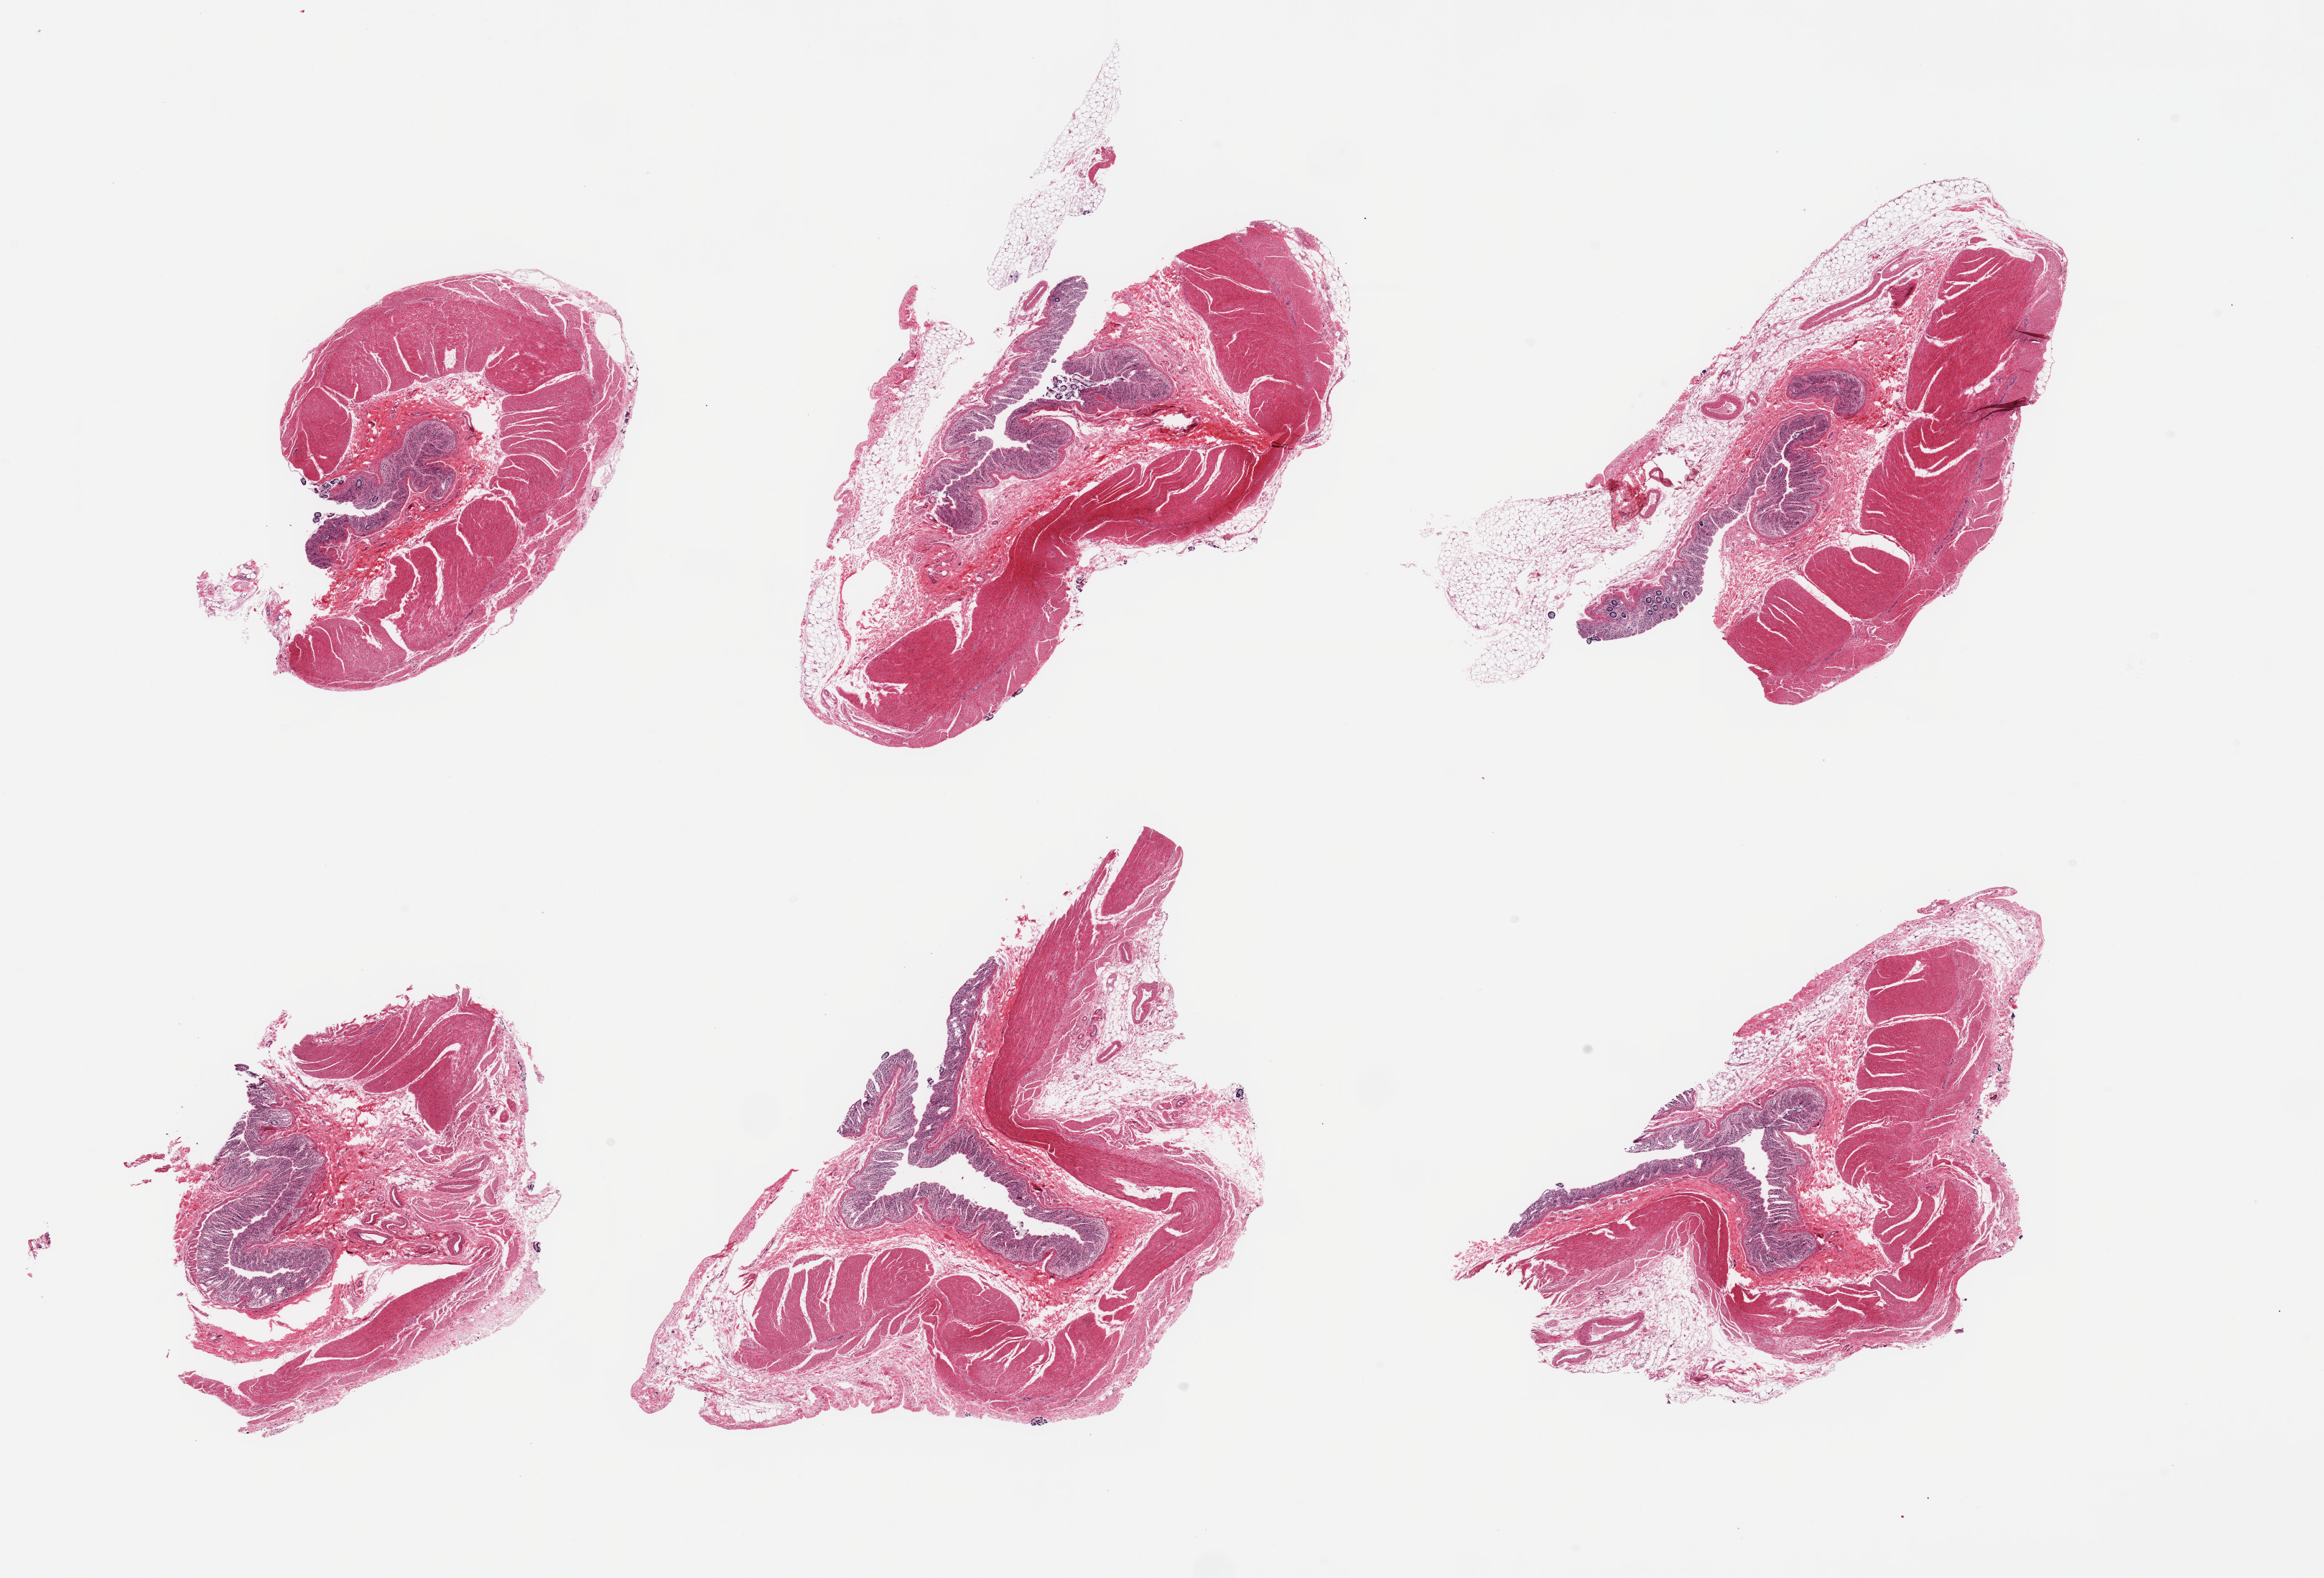
Digitized haematoxylin and eosin-stained section, shown as a low-resolution overview of the whole scanned area (about 25.6 x 17.4 mm); PAXgene-fixed, paraffin-embedded tissue; section of sigmoid colon (target tissue); donor tissue sample. Donor: male.
Reviewer comment on this tissue sample: 6 pieces; mucosa (autolyzed) present on all pieces along with muscularis.